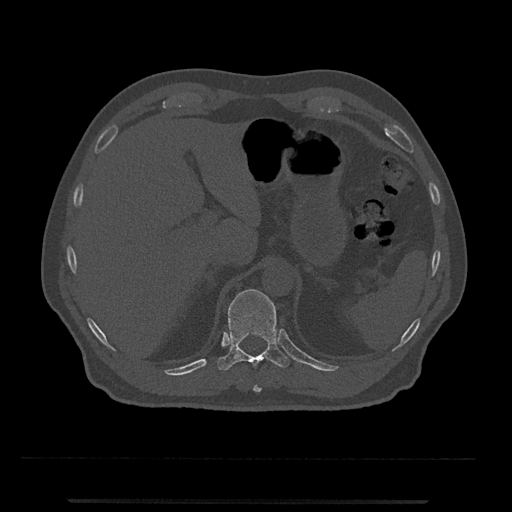
CT including the spine, one axial slice; position 471 of 797 along the scan axis; reconstruction kernel Br40s/3; 120 kVp; bone window (W 1800 / L 400 HU); 0.5 mm slice thickness; 512 × 512 image matrix. Patient: male, 63 years. Case-level facts recorded for this patient, not image findings: primary cancer: prostate.
Annotated regions visible in this slice (semi-automatically segmented with operator editing):
- T10 vertebra: bounding box <253,385,262,392> (left, top, right, bottom; pixels)
- T11 vertebra: <217,289,289,371>